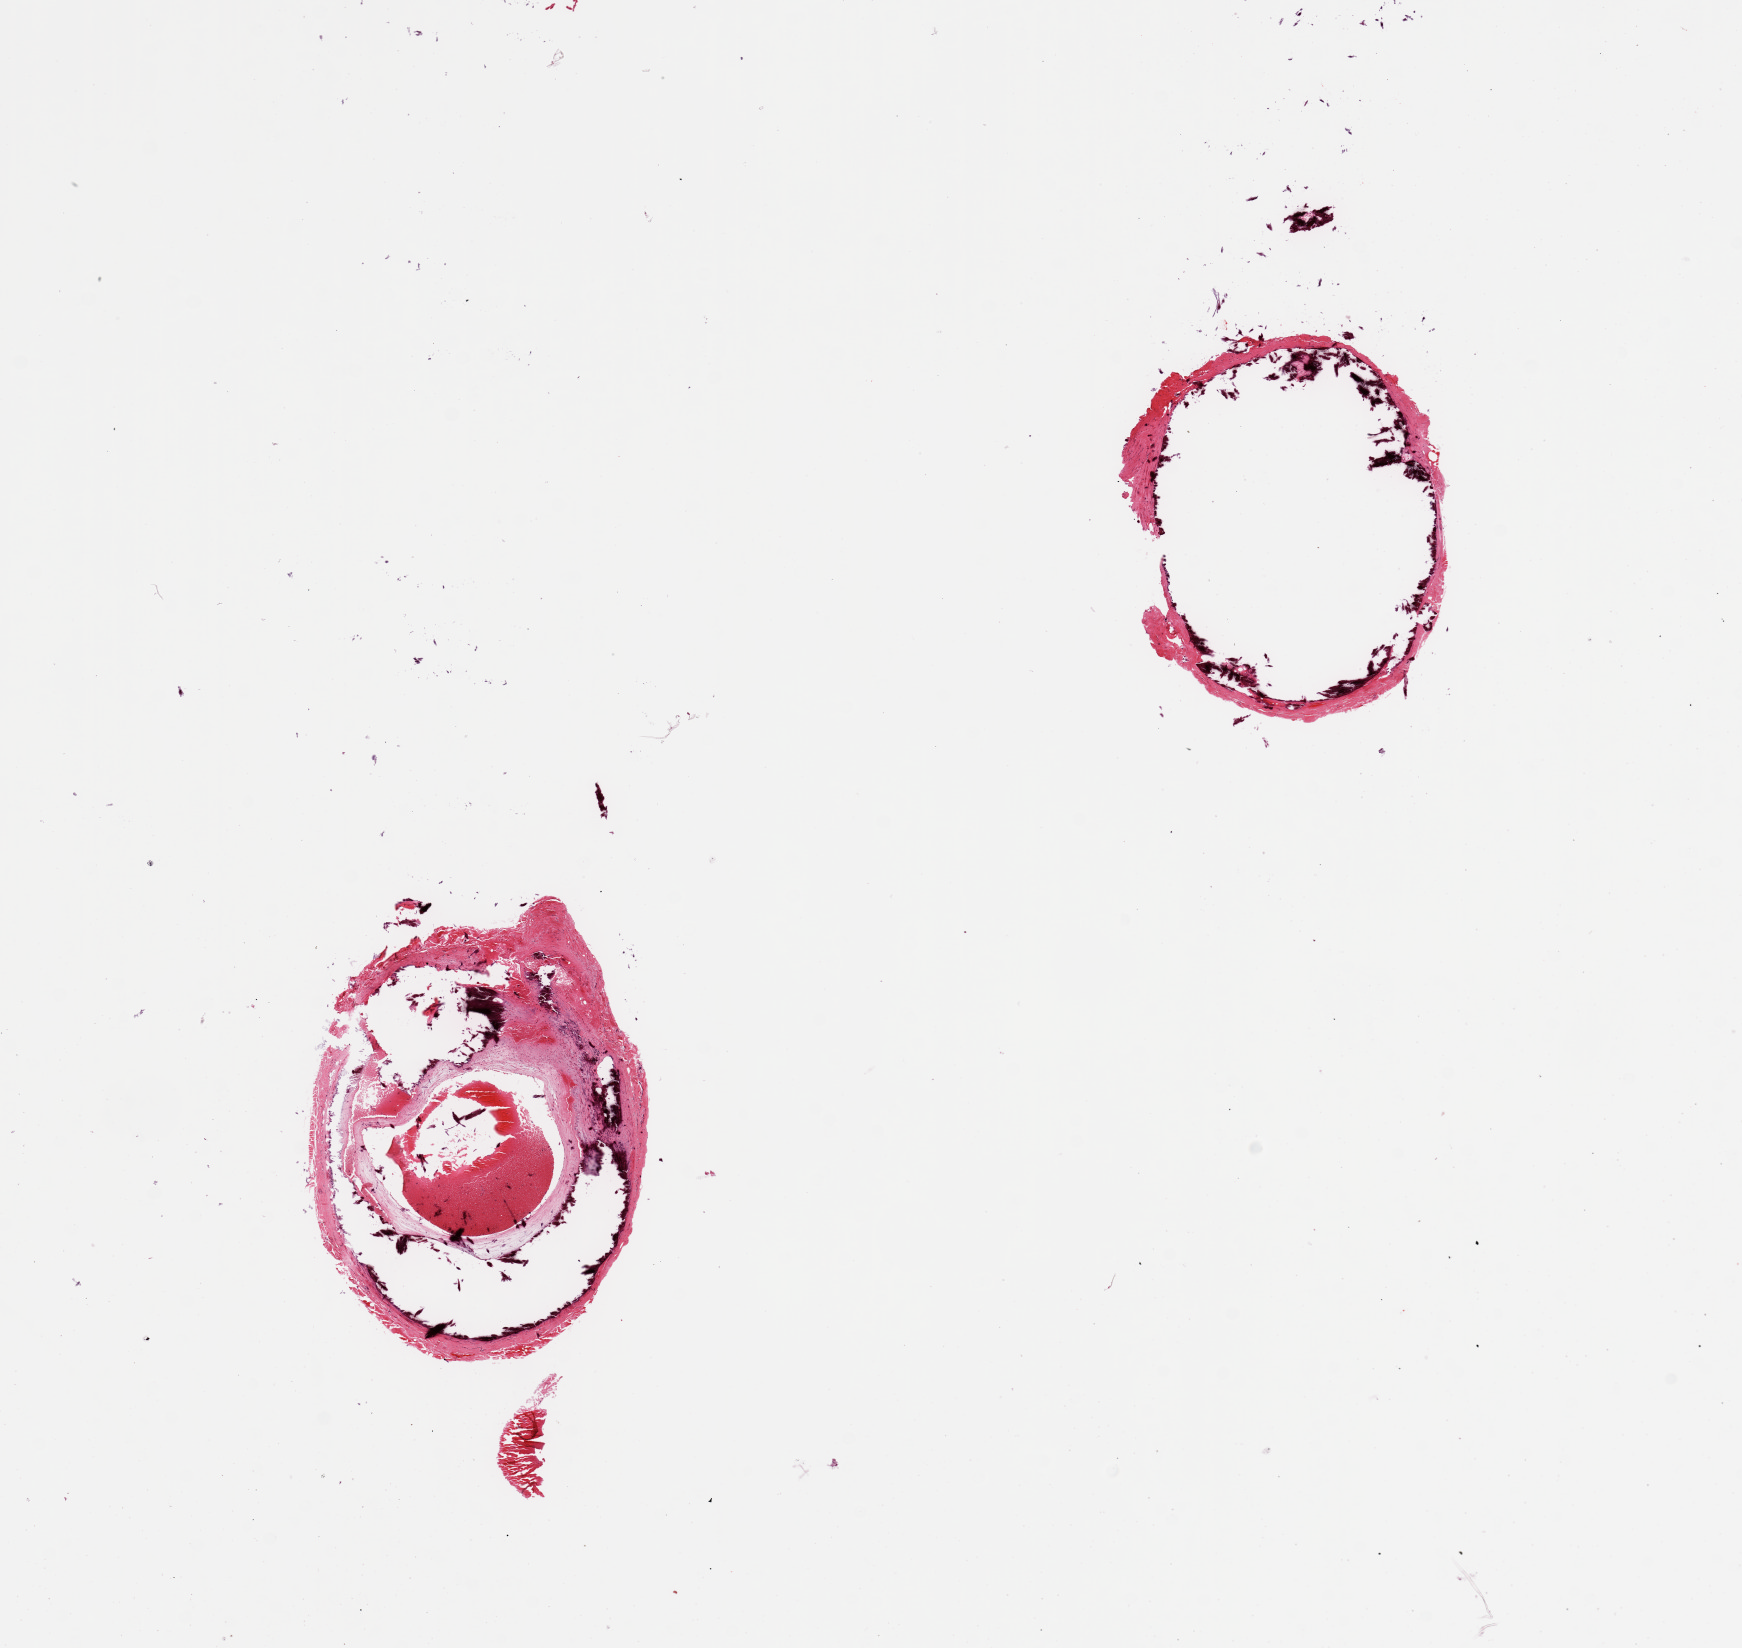
Whole-slide image, H&E stain — a low-resolution overview of the entire scanned area, about 13.8 x 13.0 mm; PAXgene-fixed, paraffin-embedded tissue; section of tibial artery (target tissue); tissue donor sample. Donor: female.
Reviewer comment on this tissue sample: 2 pieces, one piece is rim of vessel with fragments of calcified material, second is incomplete section due to severe calcific sclerosis with narrowing of the lumen.